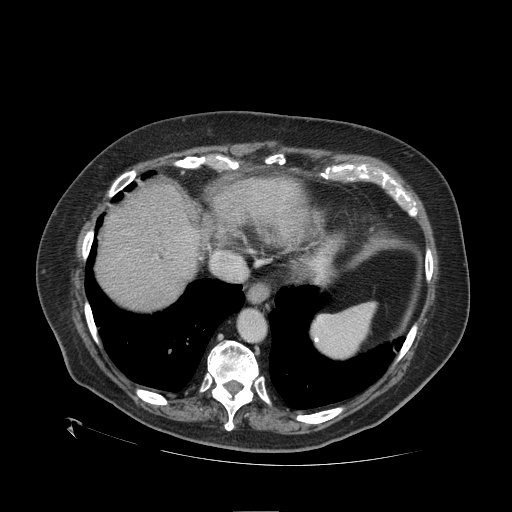
Contrast-enhanced abdominal CT (liver protocol), one axial slice. Slice 92 of 109 in the series (ordered by position). 120 kVp. One of 2 acquisitions stored at this slice position. Soft-tissue window (W 400 / L 40 HU). 512 × 512 image matrix, field of view 460 × 460 mm. From the clinical record (not read from this slice): diagnosis: hepatocellular carcinoma (patient treated with transarterial chemoembolisation; whether this scan precedes or follows treatment is not stated here); TNM stage (as recorded): Stage-I; Child-Pugh class: A; tumour differentiation: no biopsy; tumour nodularity: uninodular.
Outlined on this slice (semi-automatic segmentation, software-assisted and operator-edited):
- abdominal aorta: bounding box [x1, y1, x2, y2] px = [239, 310, 265, 340]
- liver parenchyma outside the tumour (the mass and vessels are separate outlines, so this box may not span the whole liver): [96, 178, 298, 308]